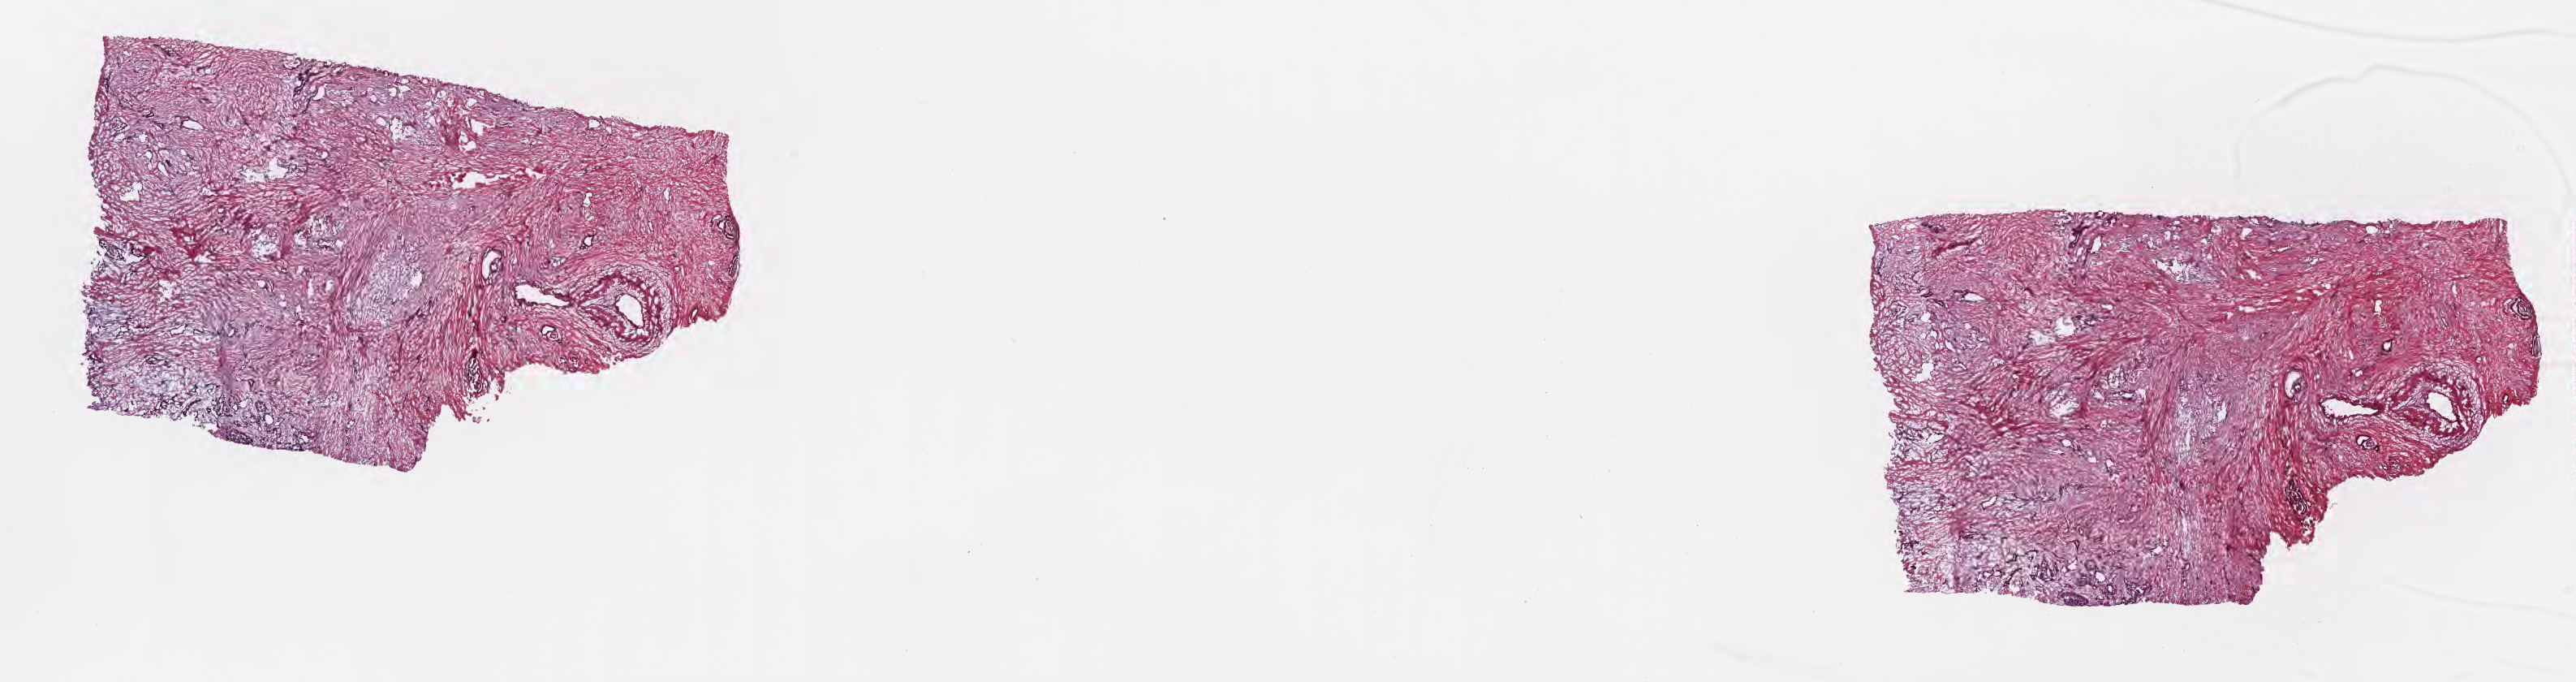
Haematoxylin and eosin whole-slide image, whole scanned area (about 25.7 x 6.8 mm) shown as a low-resolution overview. Frozen section. Primary tumor. Site: tail of pancreas. Male patient; age at initial diagnosis 39 years. Composition of this section per pathologist review: tumor cells 20%, tumor nuclei 50%, stromal cells 79%, necrosis 1%, normal cells 0%. Inflammatory infiltration, as recorded: lymphocyte infiltration 5%, monocyte infiltration 1%, neutrophil infiltration 0%.
Section: bottom of the tissue portion. Histologic diagnosis: Infiltrating duct carcinoma, NOS.